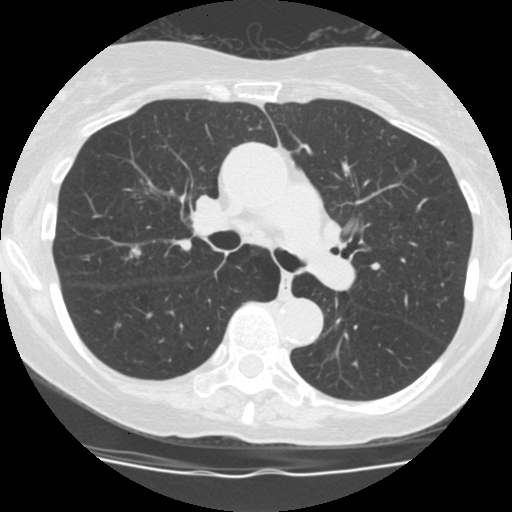
Low-dose screening chest CT, one axial slice; slice 114 of 183 in the series (ordered by position); 120 kVp; lung window (W 1500 / L -600 HU); 2.5 mm slice thickness; 512 × 512 image matrix.
Structures marked on this image (manually delineated by an expert):
- lesion 1 (tumor, upper lobe of right lung): box from (x=130, y=246) to (x=141, y=258) px